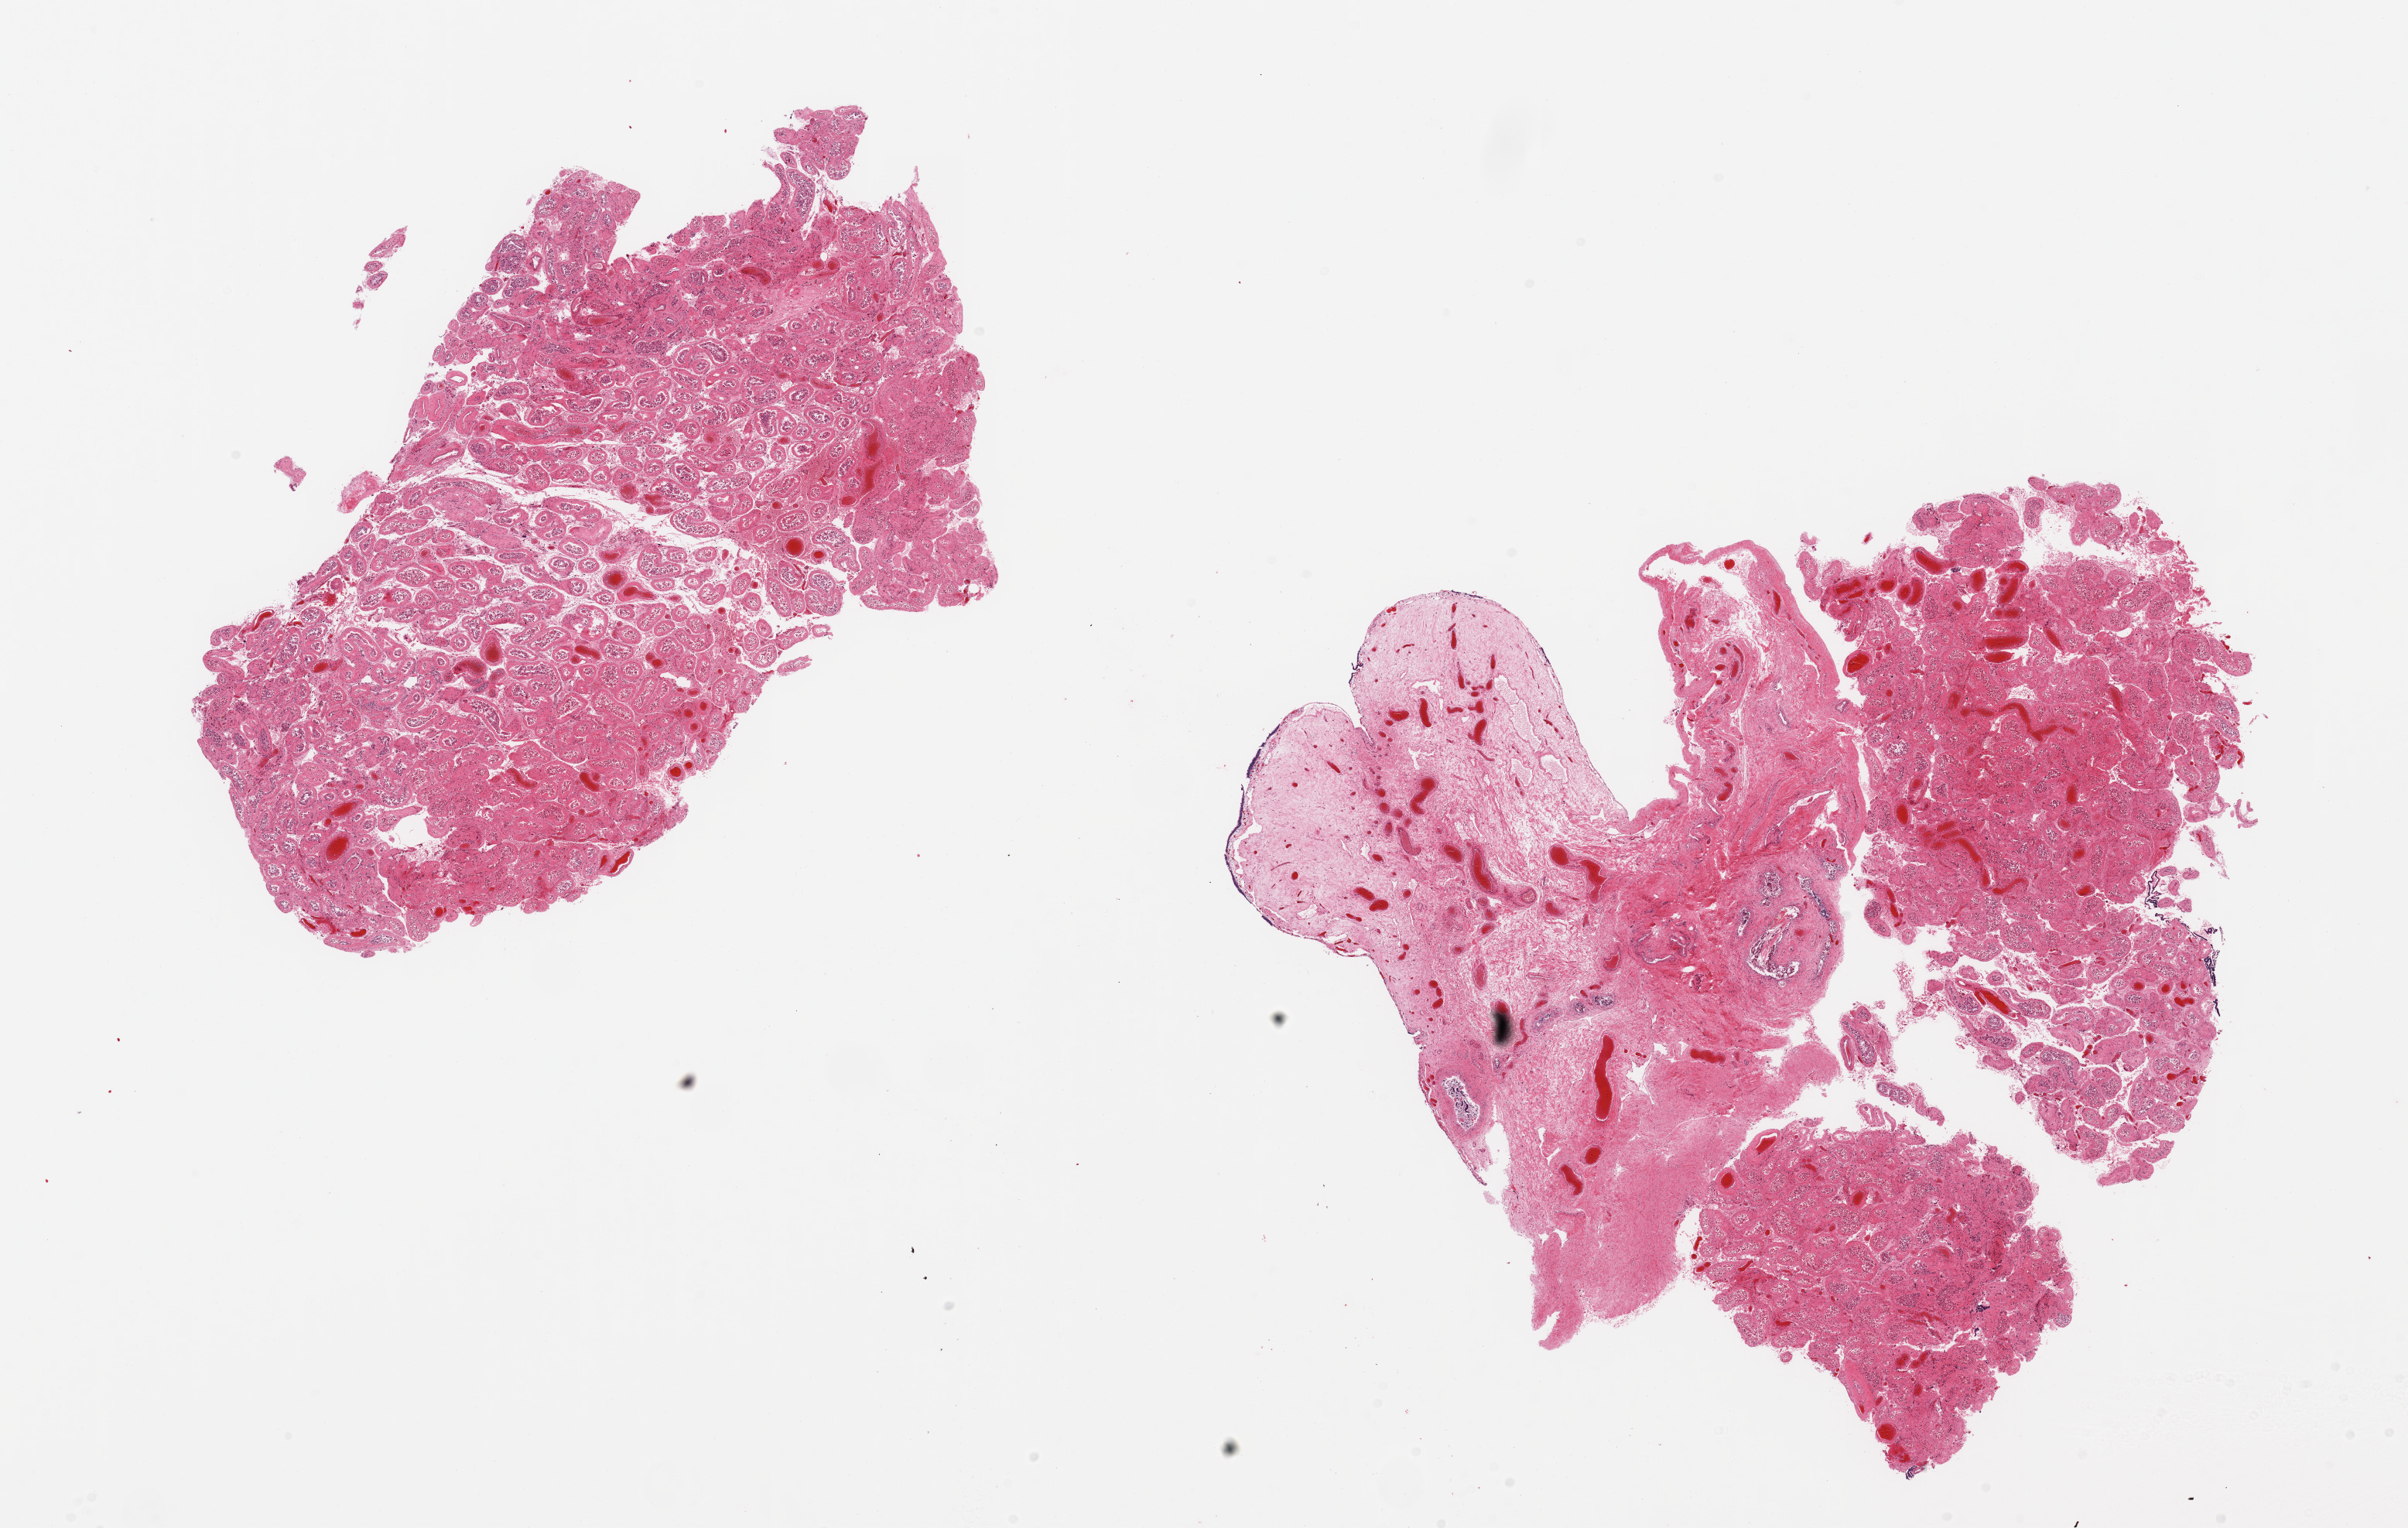
H&E whole-slide image, brightfield, low-resolution overview of the scanned area, about 24.6 x 15.6 mm (slide scanned at 20x), PAXgene-fixed, paraffin-embedded tissue, section of testis (target tissue), donor tissue sample. Donor: male.
* review note (as recorded): 2 pieces, tubular atrophy, aspermia, evidence of hemorrhagic infarction